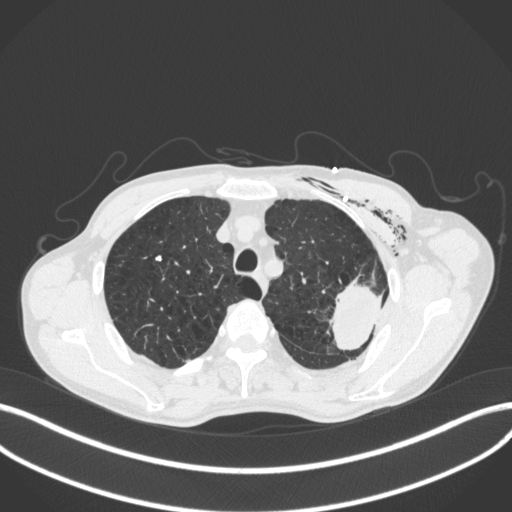
Chest CT, one axial slice; slice 327 of 416 in the series (ordered by position); reconstruction kernel B31f; lung window (W 1500 / L -600 HU); 1 mm slice thickness; 512 × 512 image matrix, field of view 400 × 400 mm. Male patient, age 58 years. From the clinical record (not read from this slice): clinical TNM (as recorded): T3 N0 M0.
Structures marked on this image (bounding box drawn by a radiologist):
- lung tumour (recorded histology: adenocarcinoma): bounding box (x1, y1, x2, y2) in pixels: (326, 279, 388, 357)